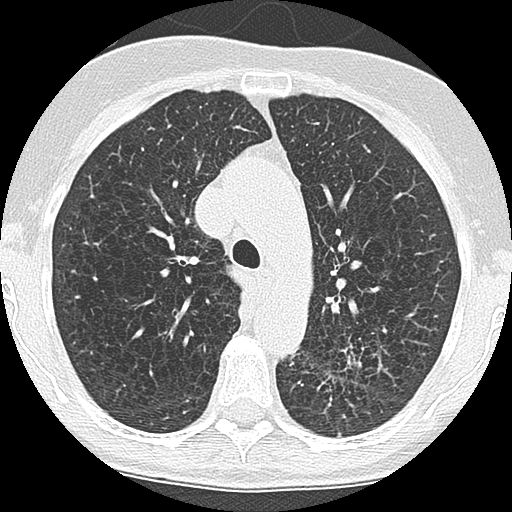
Low-dose screening chest CT, one axial slice. Slice 123 of 171 in the series (ordered by position). 120 kVp. Lung window (W 1500 / L -600 HU). 2.5 mm slice thickness. 512 × 512 image matrix, field of view 280 × 280 mm.
Structures marked on this image (expert manual segmentation):
- lesion 1 (tumor, lower lobe of left lung): bounding box [x1, y1, x2, y2] px = [341, 344, 362, 370]